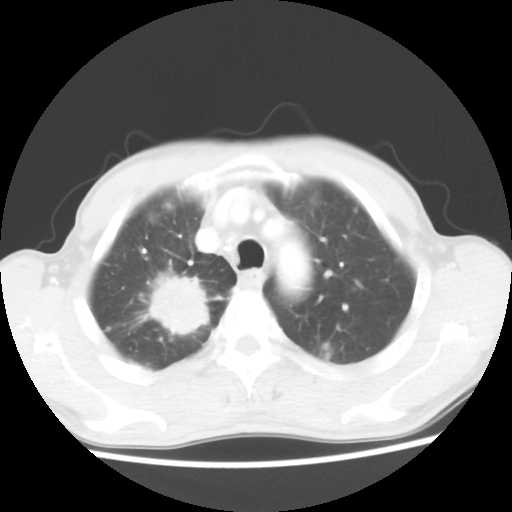
Chest CT, one axial slice. Position 42 of 52 along the scan axis. Reconstruction kernel STANDARD. Lung window (W 1500 / L -600 HU). 512 × 512 image matrix, field of view 323 × 323 mm. Male patient, age 66 years. From the clinical record (not read from this slice): clinical TNM (as recorded): T2 N0 M1a.
Annotated regions visible in this slice (rectangle marked by the reading radiologist):
- lung tumour (recorded histology: adenocarcinoma): bounding box <130,265,219,336> (left, top, right, bottom; pixels)